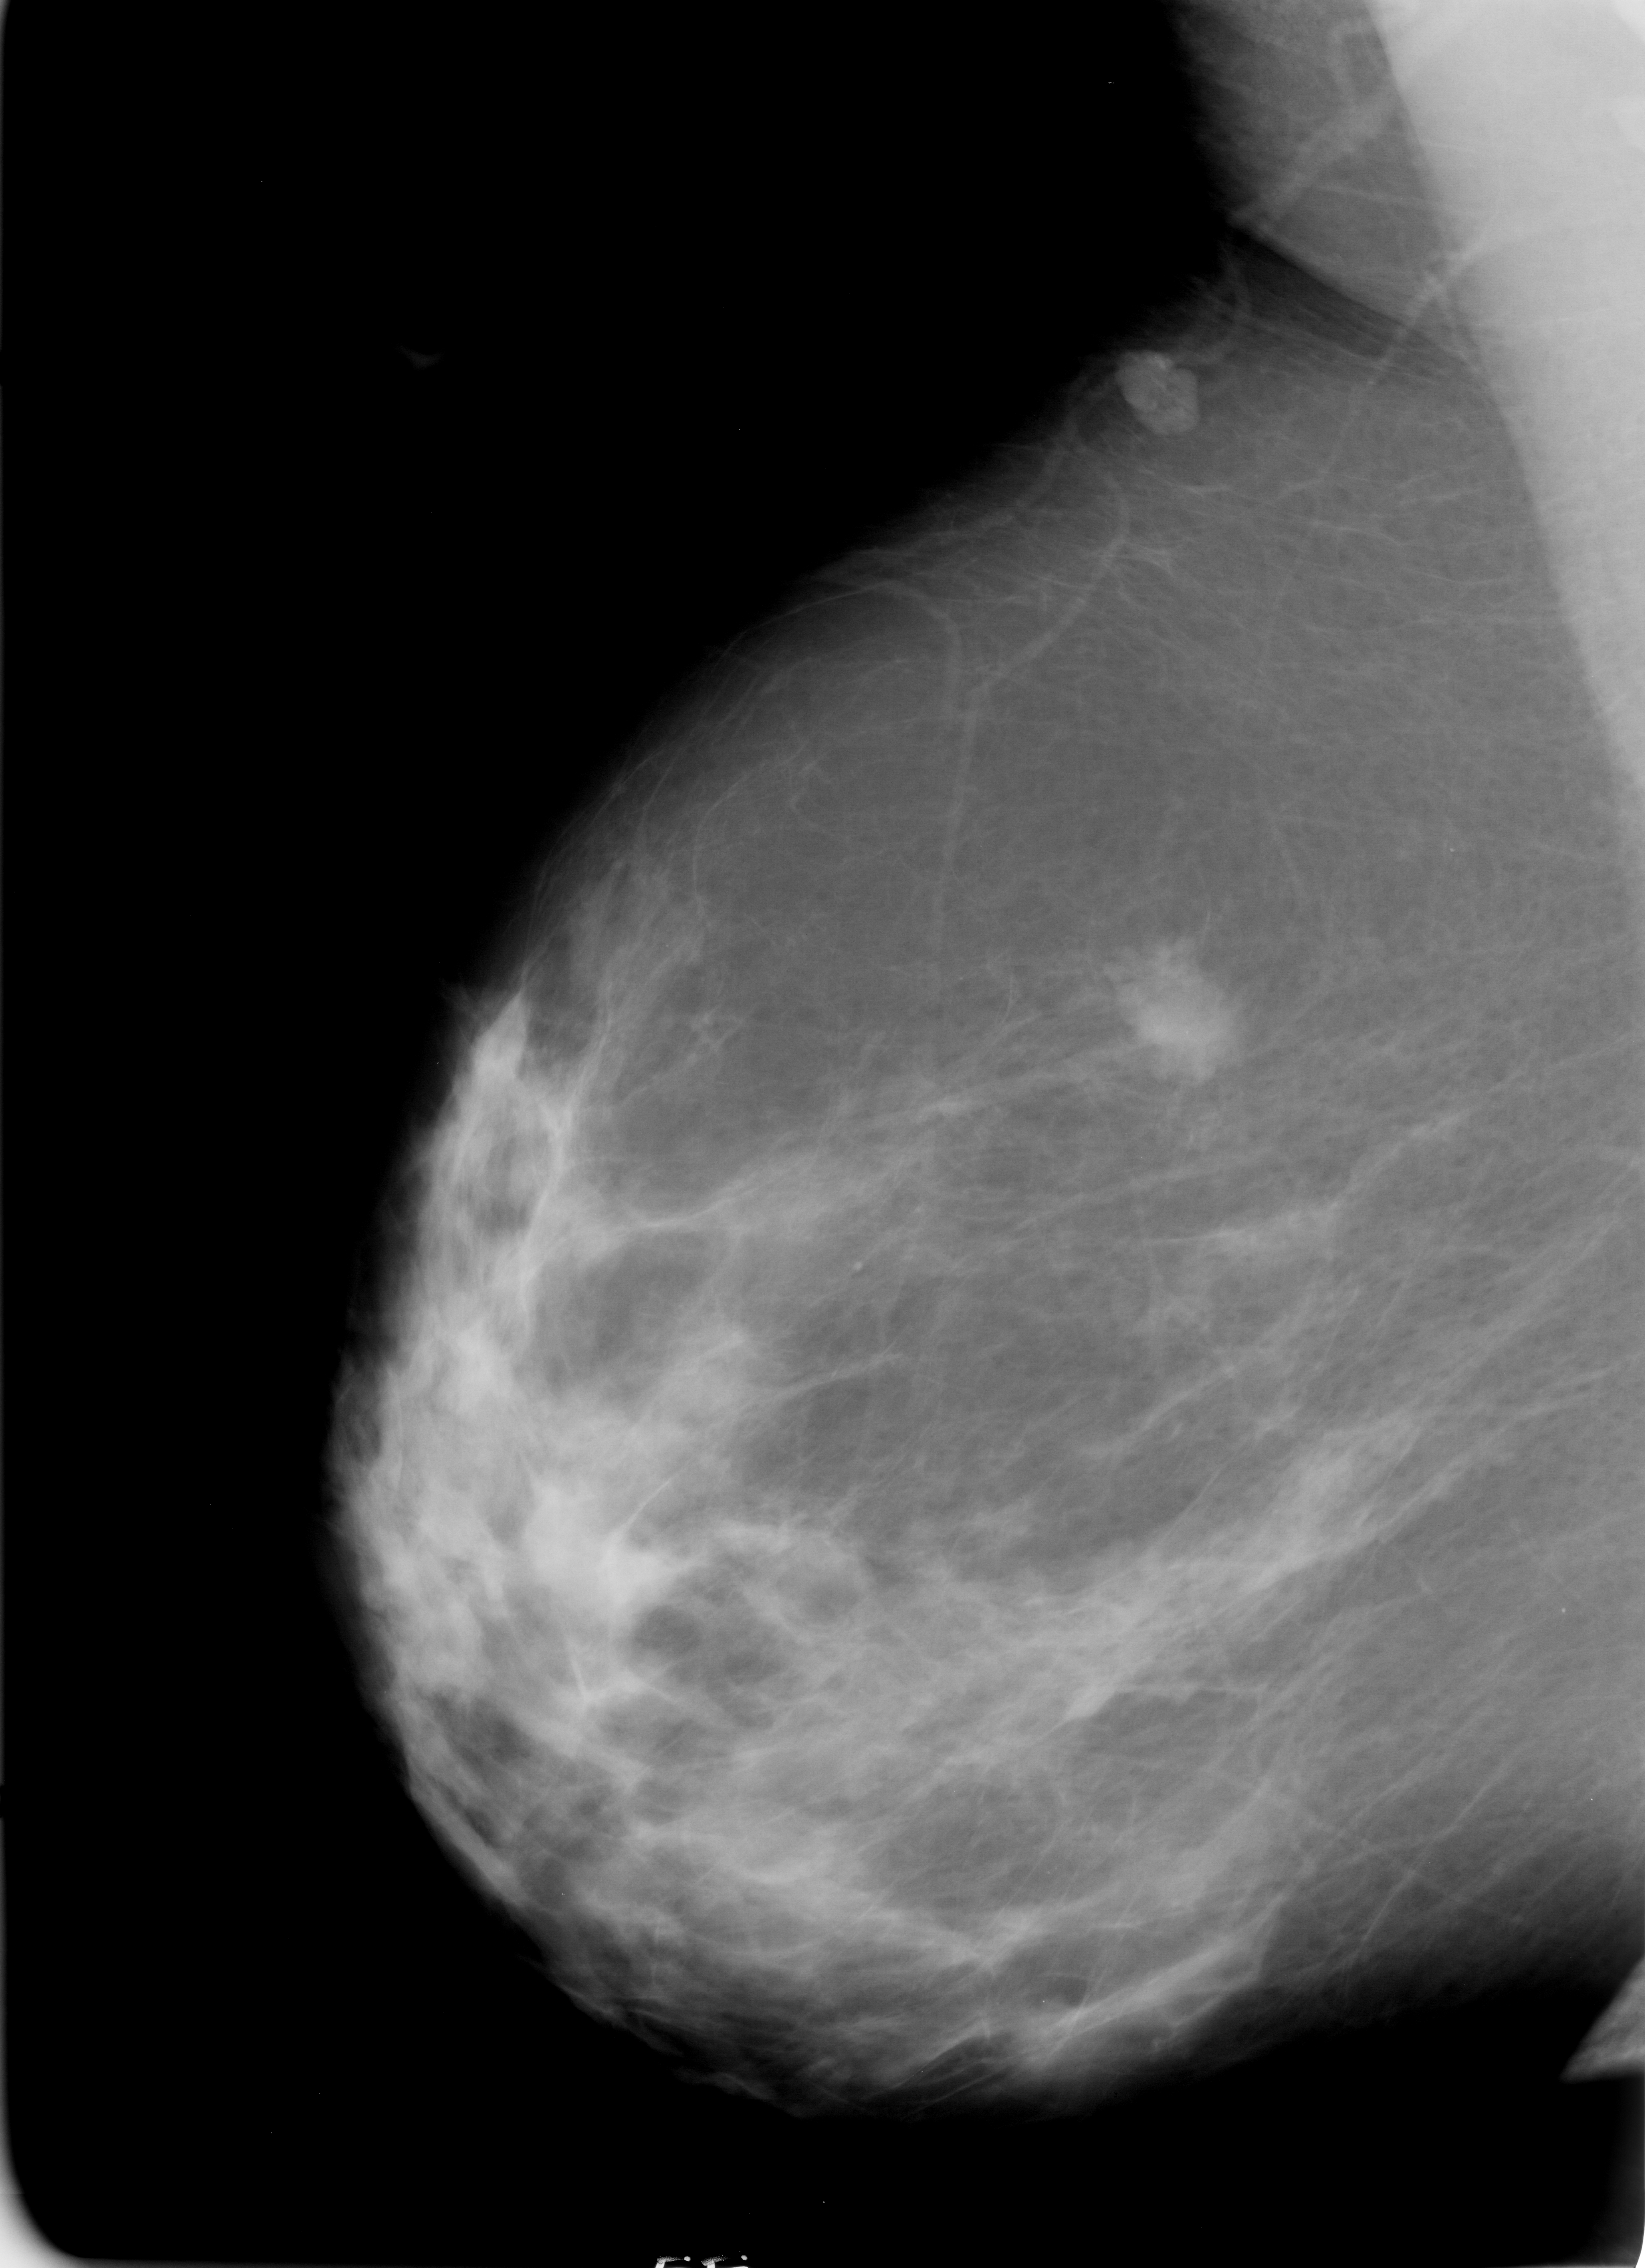
Scanned film-screen mammogram, right breast, mediolateral oblique (MLO) view, BI-RADS breast density category 2 (scale 1–4).
Abnormality record for this image: mass, shape lobulated, margins circumscribed / ill defined; BI-RADS assessment category 4; subtlety rating 4 on a 1 (subtle) to 5 (obvious) scale; pathology result (as recorded, not read from the image): malignant.